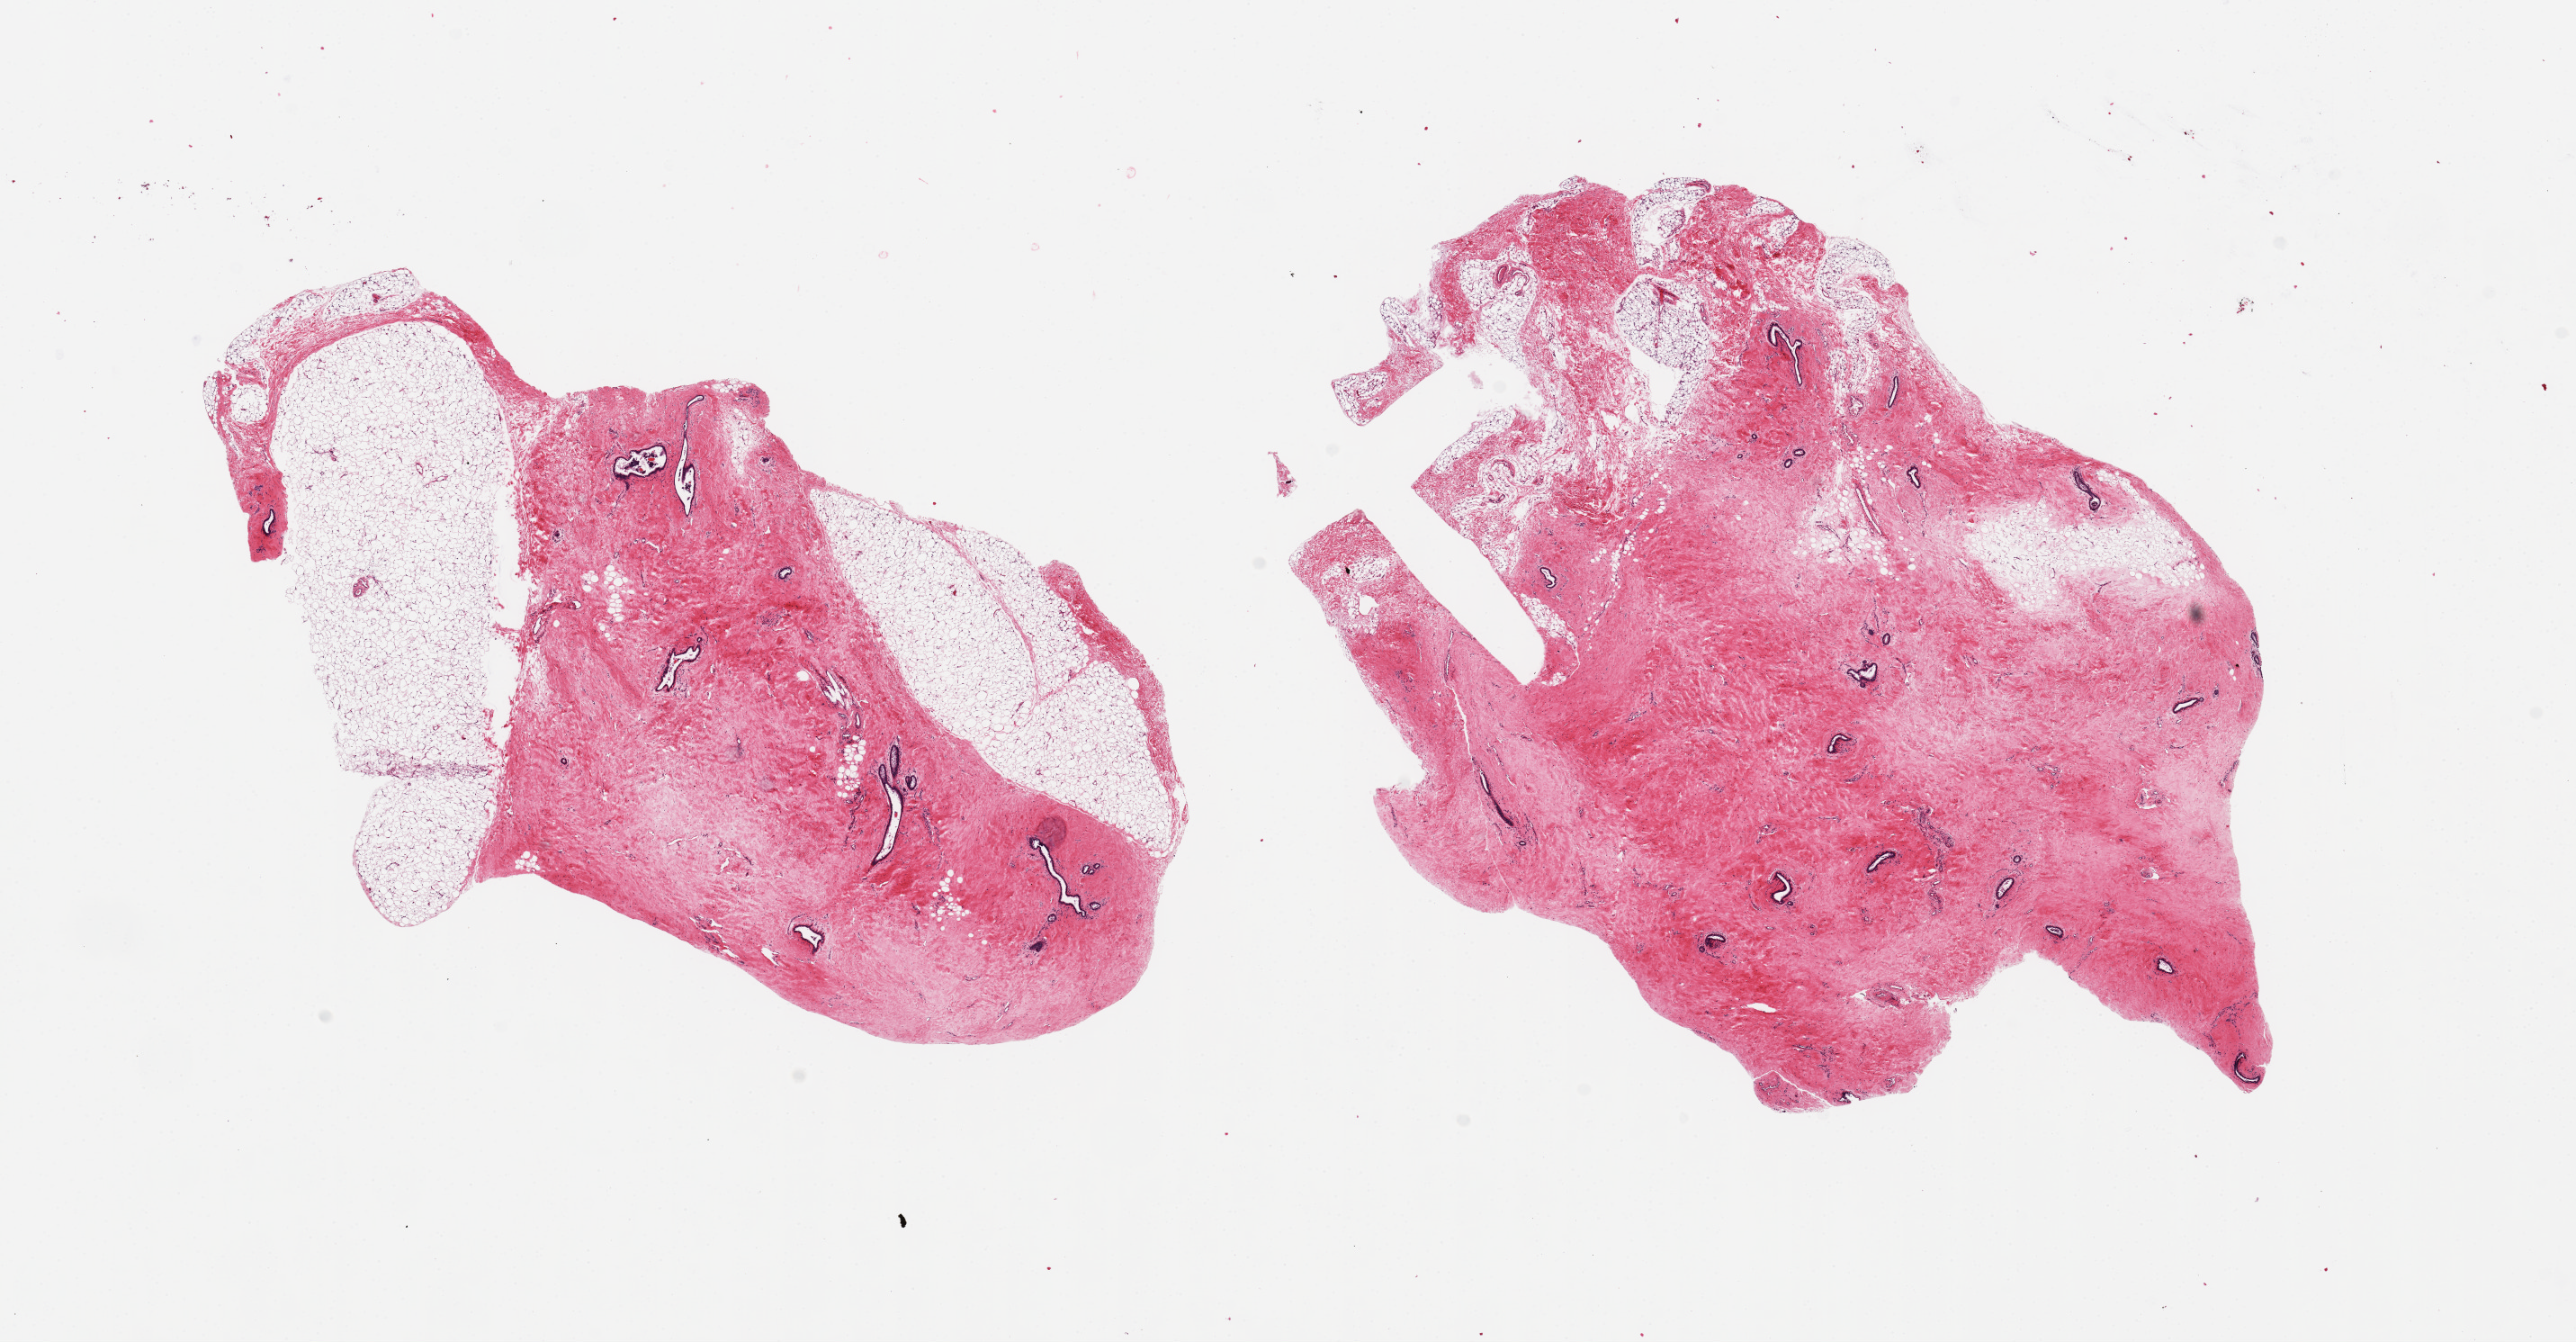
Whole-slide image, haematoxylin and eosin stain, brightfield, whole scanned area (about 22.6 x 11.8 mm, from a 20x scan) shown as a low-resolution overview; PAXgene-fixed paraffin-embedded (PFPE) section; sampled site (target tissue): breast; donor tissue sample. Male donor.
Review note (as recorded): 2 pieces up to 10x6 mm; ducts; ~30% adipose.